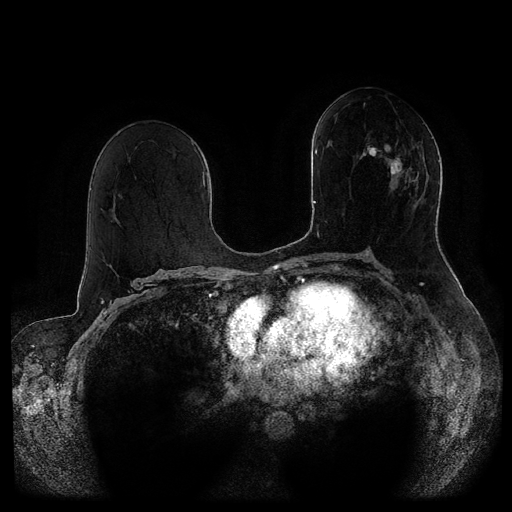
Breast MRI (dynamic contrast-enhanced, multi-phase), one axial slice; slice 51 of 116 in the series (ordered by position); dynamic contrast-enhanced series, time point 2 of 5 at this slice position (early post-contrast); 1.5 T; TE 2.6 ms, TR 5.3 ms; 2 mm slice thickness; 512 × 512 image matrix. Female patient, age 51 years.
Annotated regions visible in this slice (semi-automatic segmentation, software-assisted and operator-edited):
- breast lesion (labelled 'tumour' in the annotation; benign lesions carry a separate 'benign' label): bounding box [x1, y1, x2, y2] px = [360, 139, 410, 183]